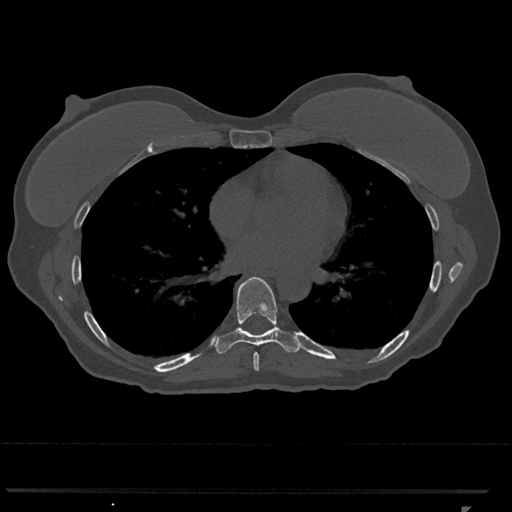
CT including the spine, one axial slice; position 670 of 793 along the scan axis; 120 kVp; bone window (W 1800 / L 400 HU); 512 × 512 image matrix, field of view 380 × 380 mm. Female patient, age 62 years. From the clinical record (not read from this slice): primary cancer: renal.
Structures marked on this image (semi-automatic segmentation, software-assisted and operator-edited):
- T7 vertebra: bounding box (x1, y1, x2, y2) in pixels: (253, 353, 259, 371)
- T8 vertebra: (215, 277, 299, 354)